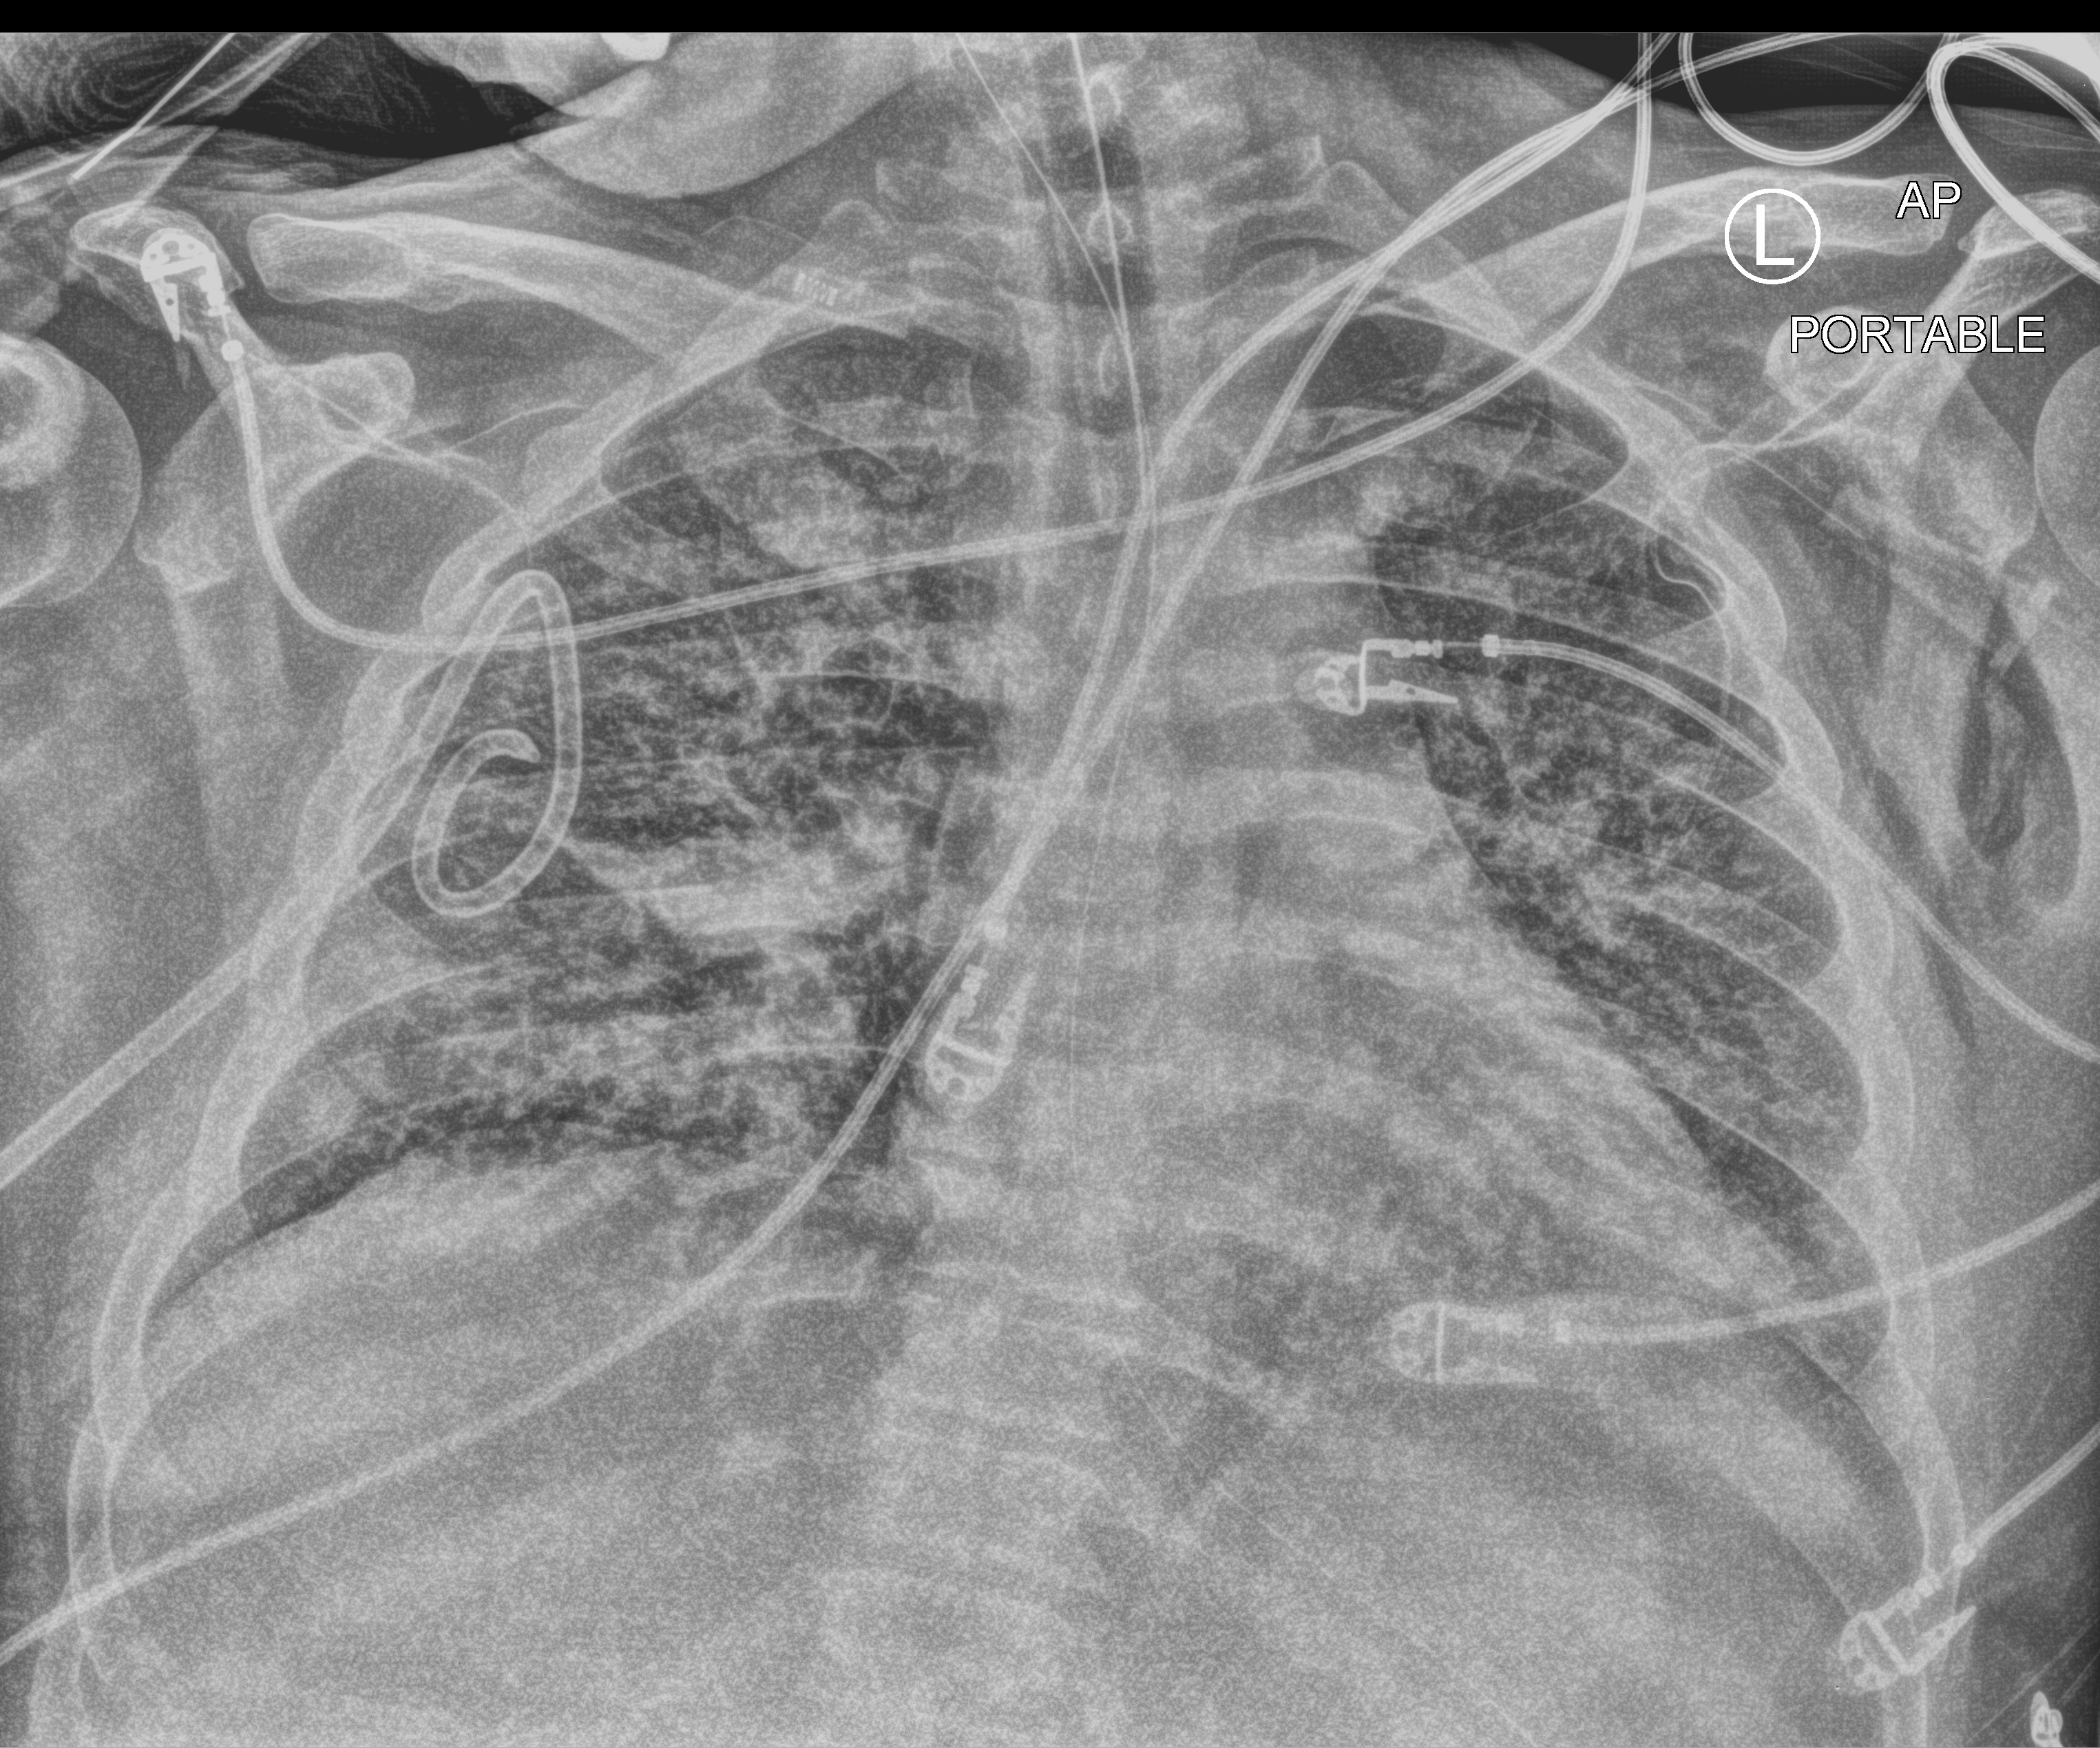
Portable chest radiograph, anteroposterior (AP) projection. Adult patient hospitalised with COVID-19, age 18–59 years.
Admission-level facts for this patient (not findings on this image; timing relative to this image not recorded): length of hospital stay: 31 days.